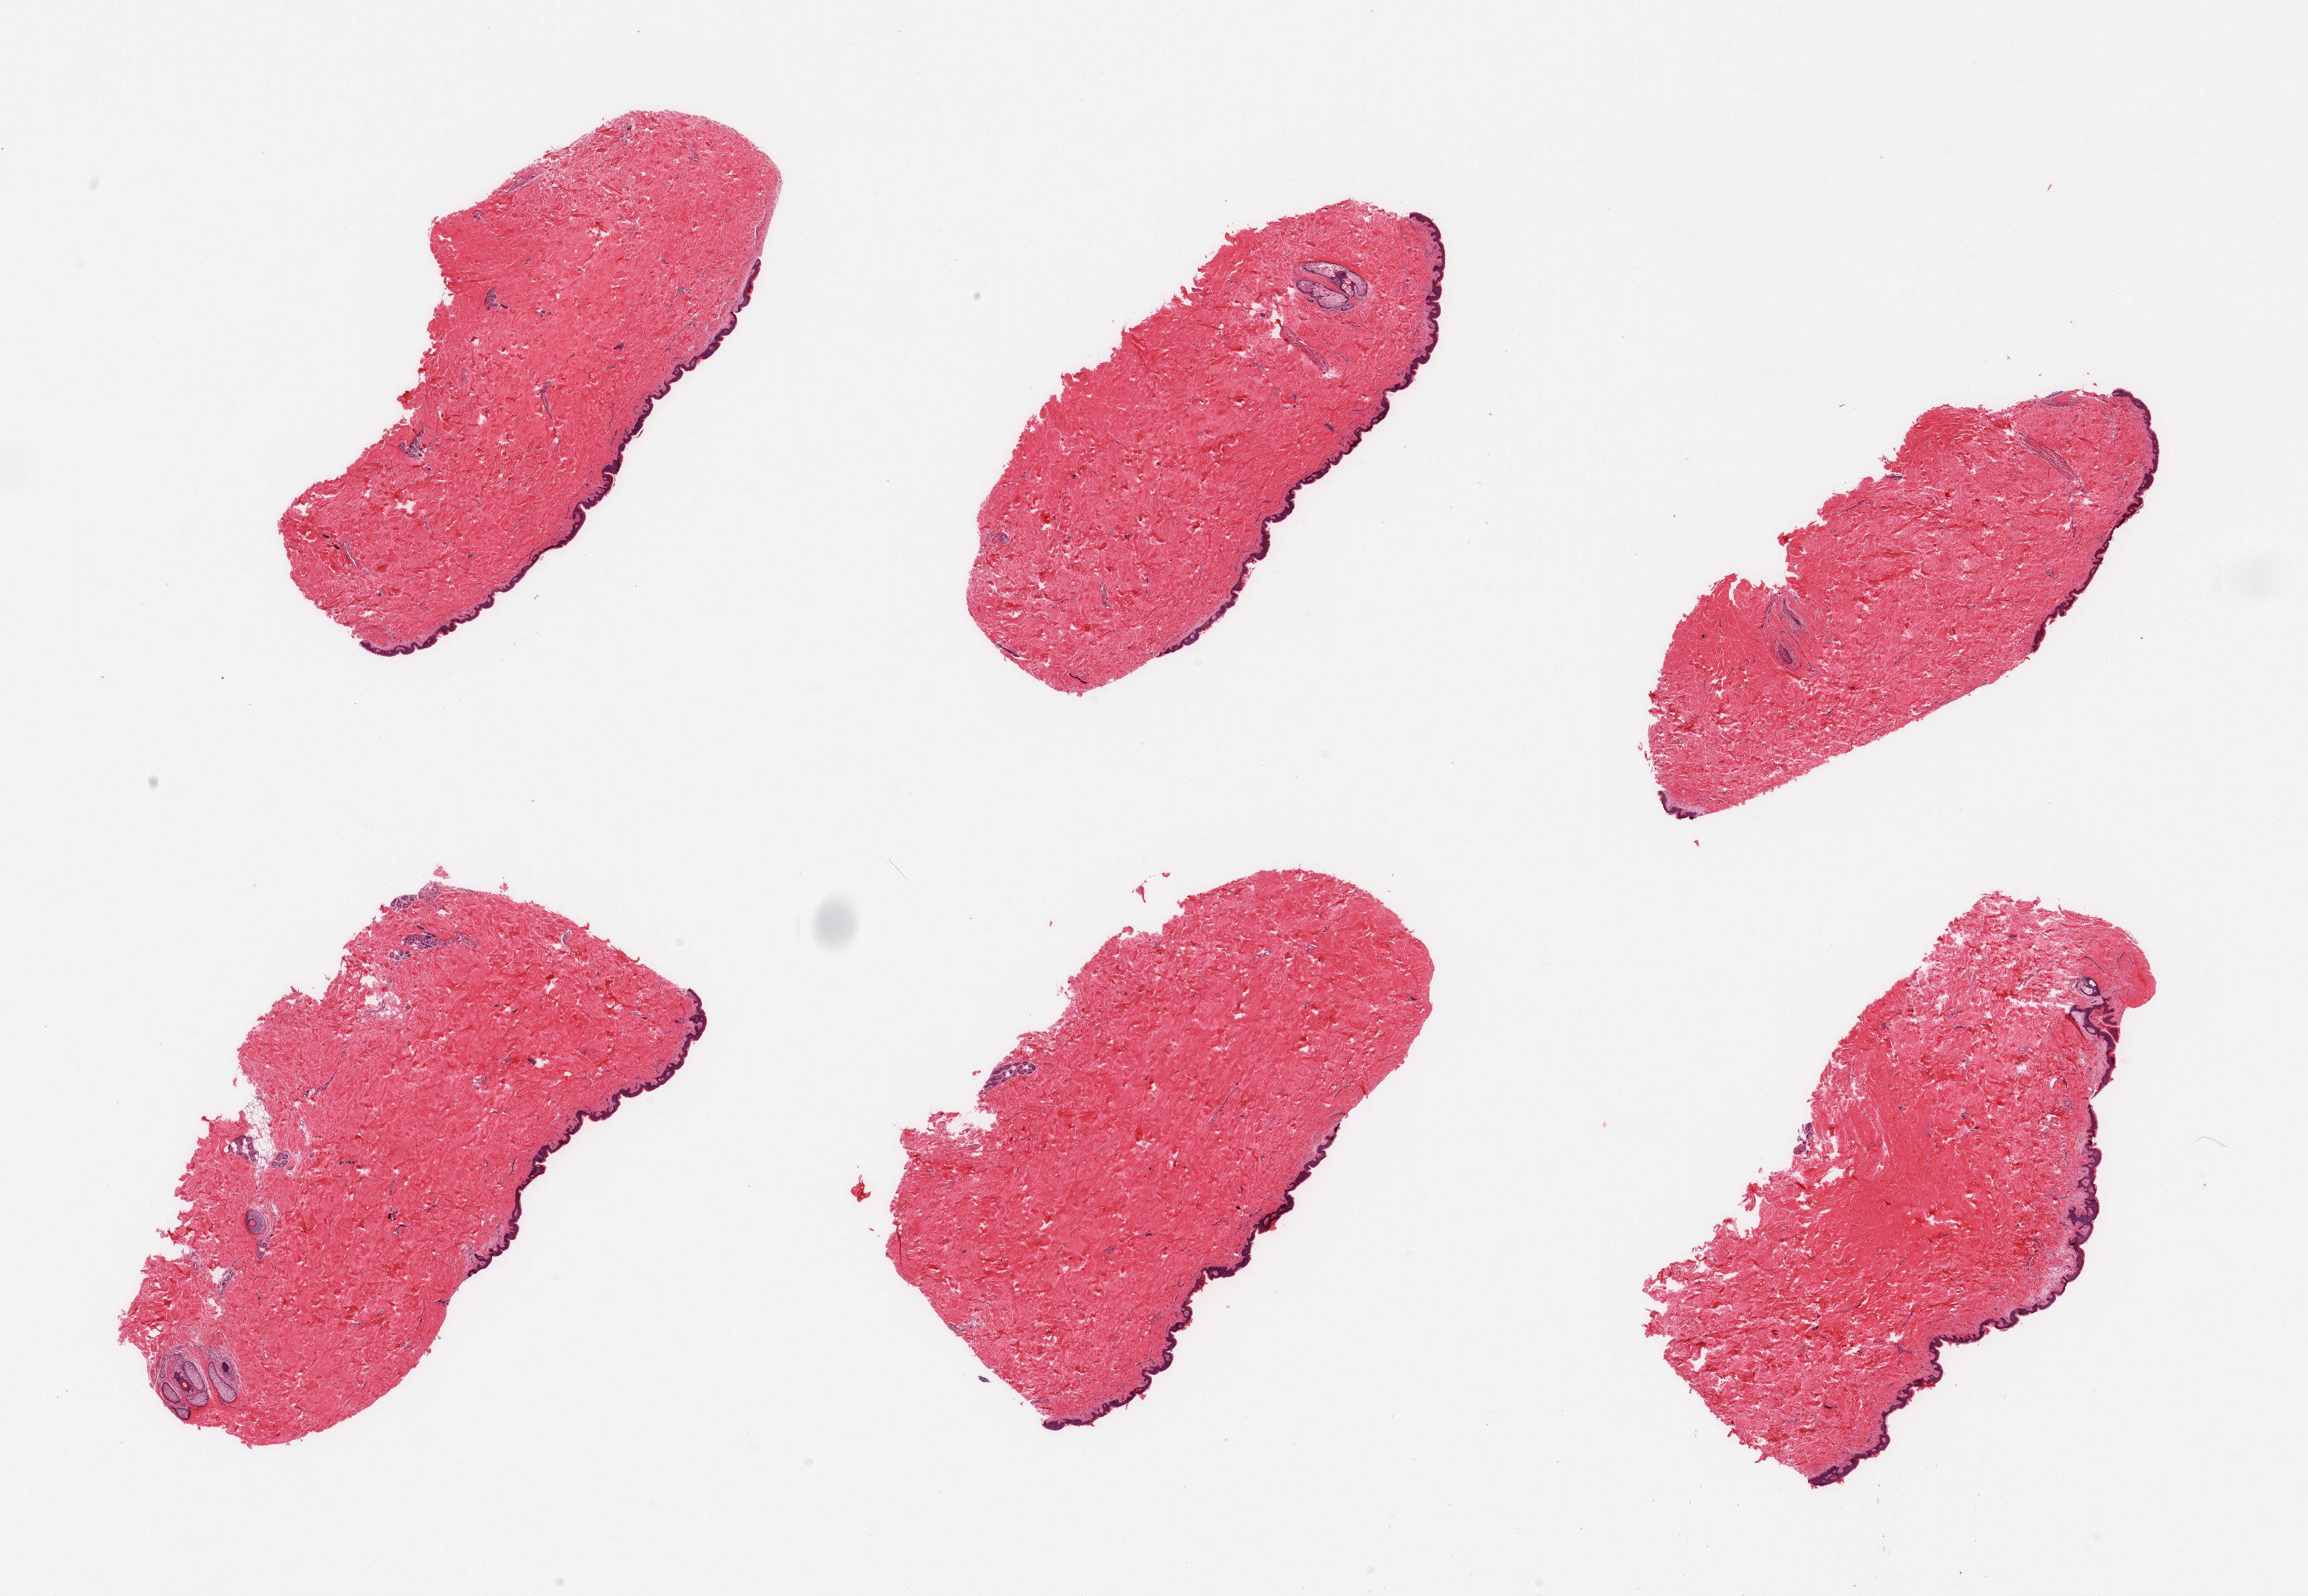
Digitized hematoxylin and eosin (H&E)-stained section — low-resolution overview of the scanned area, about 25.6 x 17.7 mm. PAXgene-fixed, paraffin-embedded tissue. Target tissue: skin of suprapubic region. Tissue donor sample. Male donor.
• reviewer comment on this tissue sample: 6 pieces, no dermal fat; squamous epithelium is ~40-50 microns